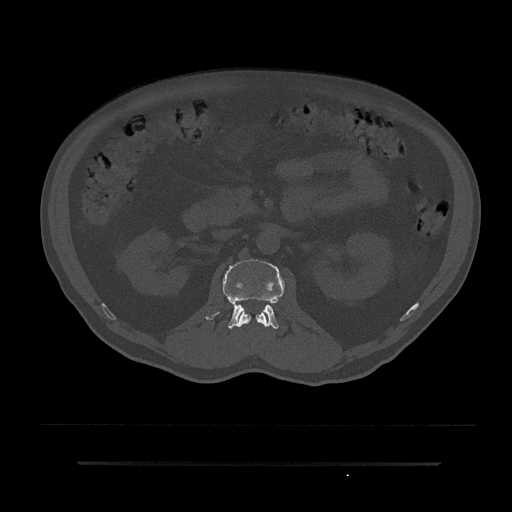
CT including the spine, one axial slice; slice 102 of 797 in the series (ordered by position); reconstruction kernel Br40s/3; 120 kVp; bone window (W 1800 / L 400 HU); 0.5 mm slice thickness; 512 × 512 image matrix, field of view 464 × 464 mm. Patient: male, 59 years. From the clinical record (not read from this slice): primary cancer: bile ducts; vertebrae with lytic lesions (as recorded): T10.
Annotated regions visible in this slice (semi-automatic segmentation, software-assisted and operator-edited):
- L1 vertebra: bounding box <237,311,267,327> (left, top, right, bottom; pixels)
- L2 vertebra: <206,259,284,329>